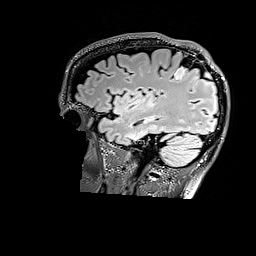
Brain MRI from a brain-tumour surgery series, one sagittal slice. Position 125 of 176 along the scan axis. T2 FLAIR. 256 × 256 image matrix, field of view 256 × 256 mm. From the clinical record (not read from this slice): histopathology: Astrocytoma; WHO grade: 3; IDH mutation: yes.
Structures marked on this image (manually delineated by an expert):
- tumour: box from (x=175, y=66) to (x=188, y=79) px